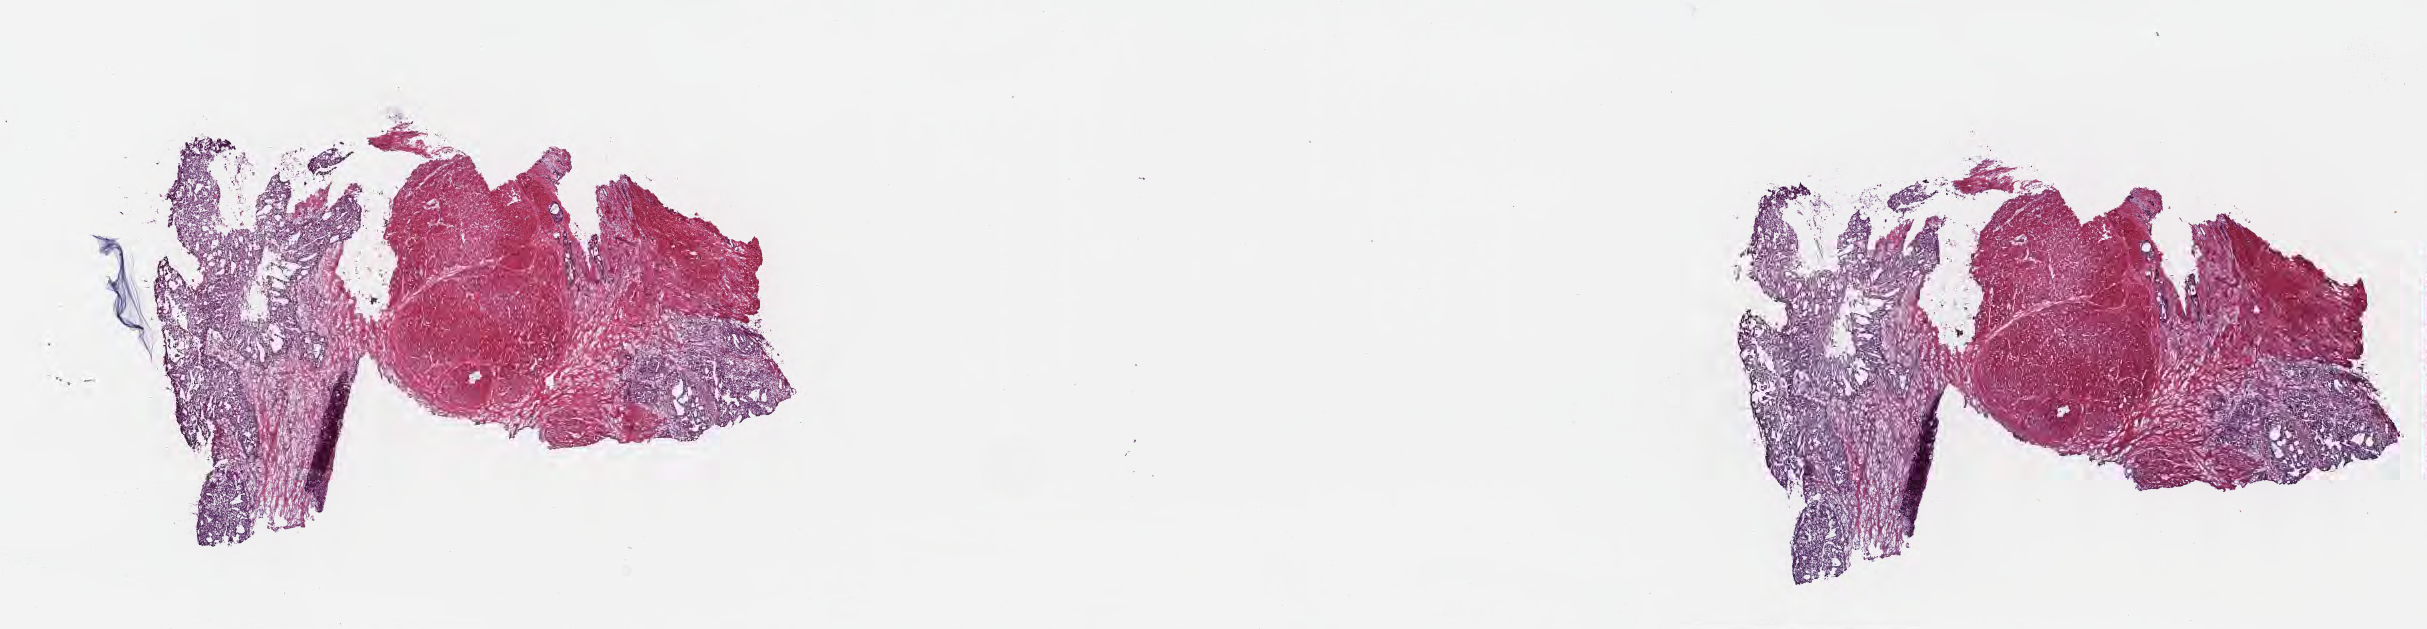
Whole-slide image, haematoxylin and eosin stain — a low-resolution overview of the entire scanned area, about 19.6 x 5.1 mm; frozen section (tissue freezing medium); primary tumor; anatomic site: head of pancreas. Male, age 72 years at initial diagnosis. Tumor grade: G2 (moderately differentiated). Composition of this section per pathologist review: tumor cells 34%, tumor nuclei 88%, stromal cells 65%, necrosis 1%, normal cells 0%. Inflammatory infiltration, as recorded: lymphocyte infiltration 8%, monocyte infiltration 1%, neutrophil infiltration 0%.
• histologic diagnosis: Intraductal papillary mucinous neoplasm with invasive carcinoma
• AJCC pathologic stage: Stage III
• section: top of the tissue portion